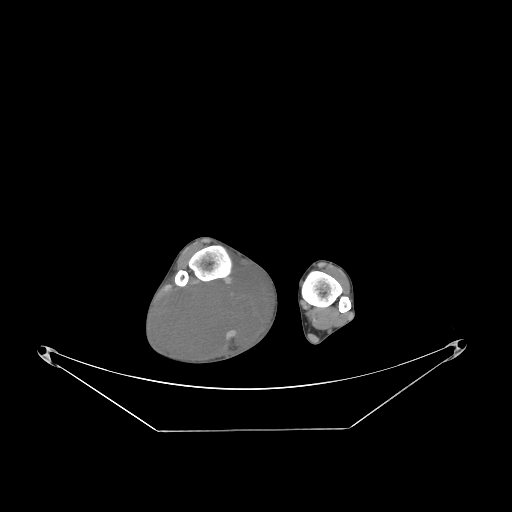
CT of an extremity soft-tissue mass (from a PET/CT study), one axial slice. Slice 55 of 267 in the series (ordered by position). Reconstruction kernel STANDARD. 140 kVp. Soft-tissue window (W 400 / L 40 HU). 3.75 mm slice thickness. 512 × 512 image matrix, field of view 500 × 500 mm. Male patient. Case-level facts recorded for this patient, not image findings: histological type: liposarcoma - round cell; grade: high; site of the primary tumour: right calf.
Annotated regions visible in this slice (expert contour drawn on MRI and transferred to this co-registered scan by the dataset authors):
- gross tumour volume (mass): bounding box [x1, y1, x2, y2] px = [158, 269, 275, 364]